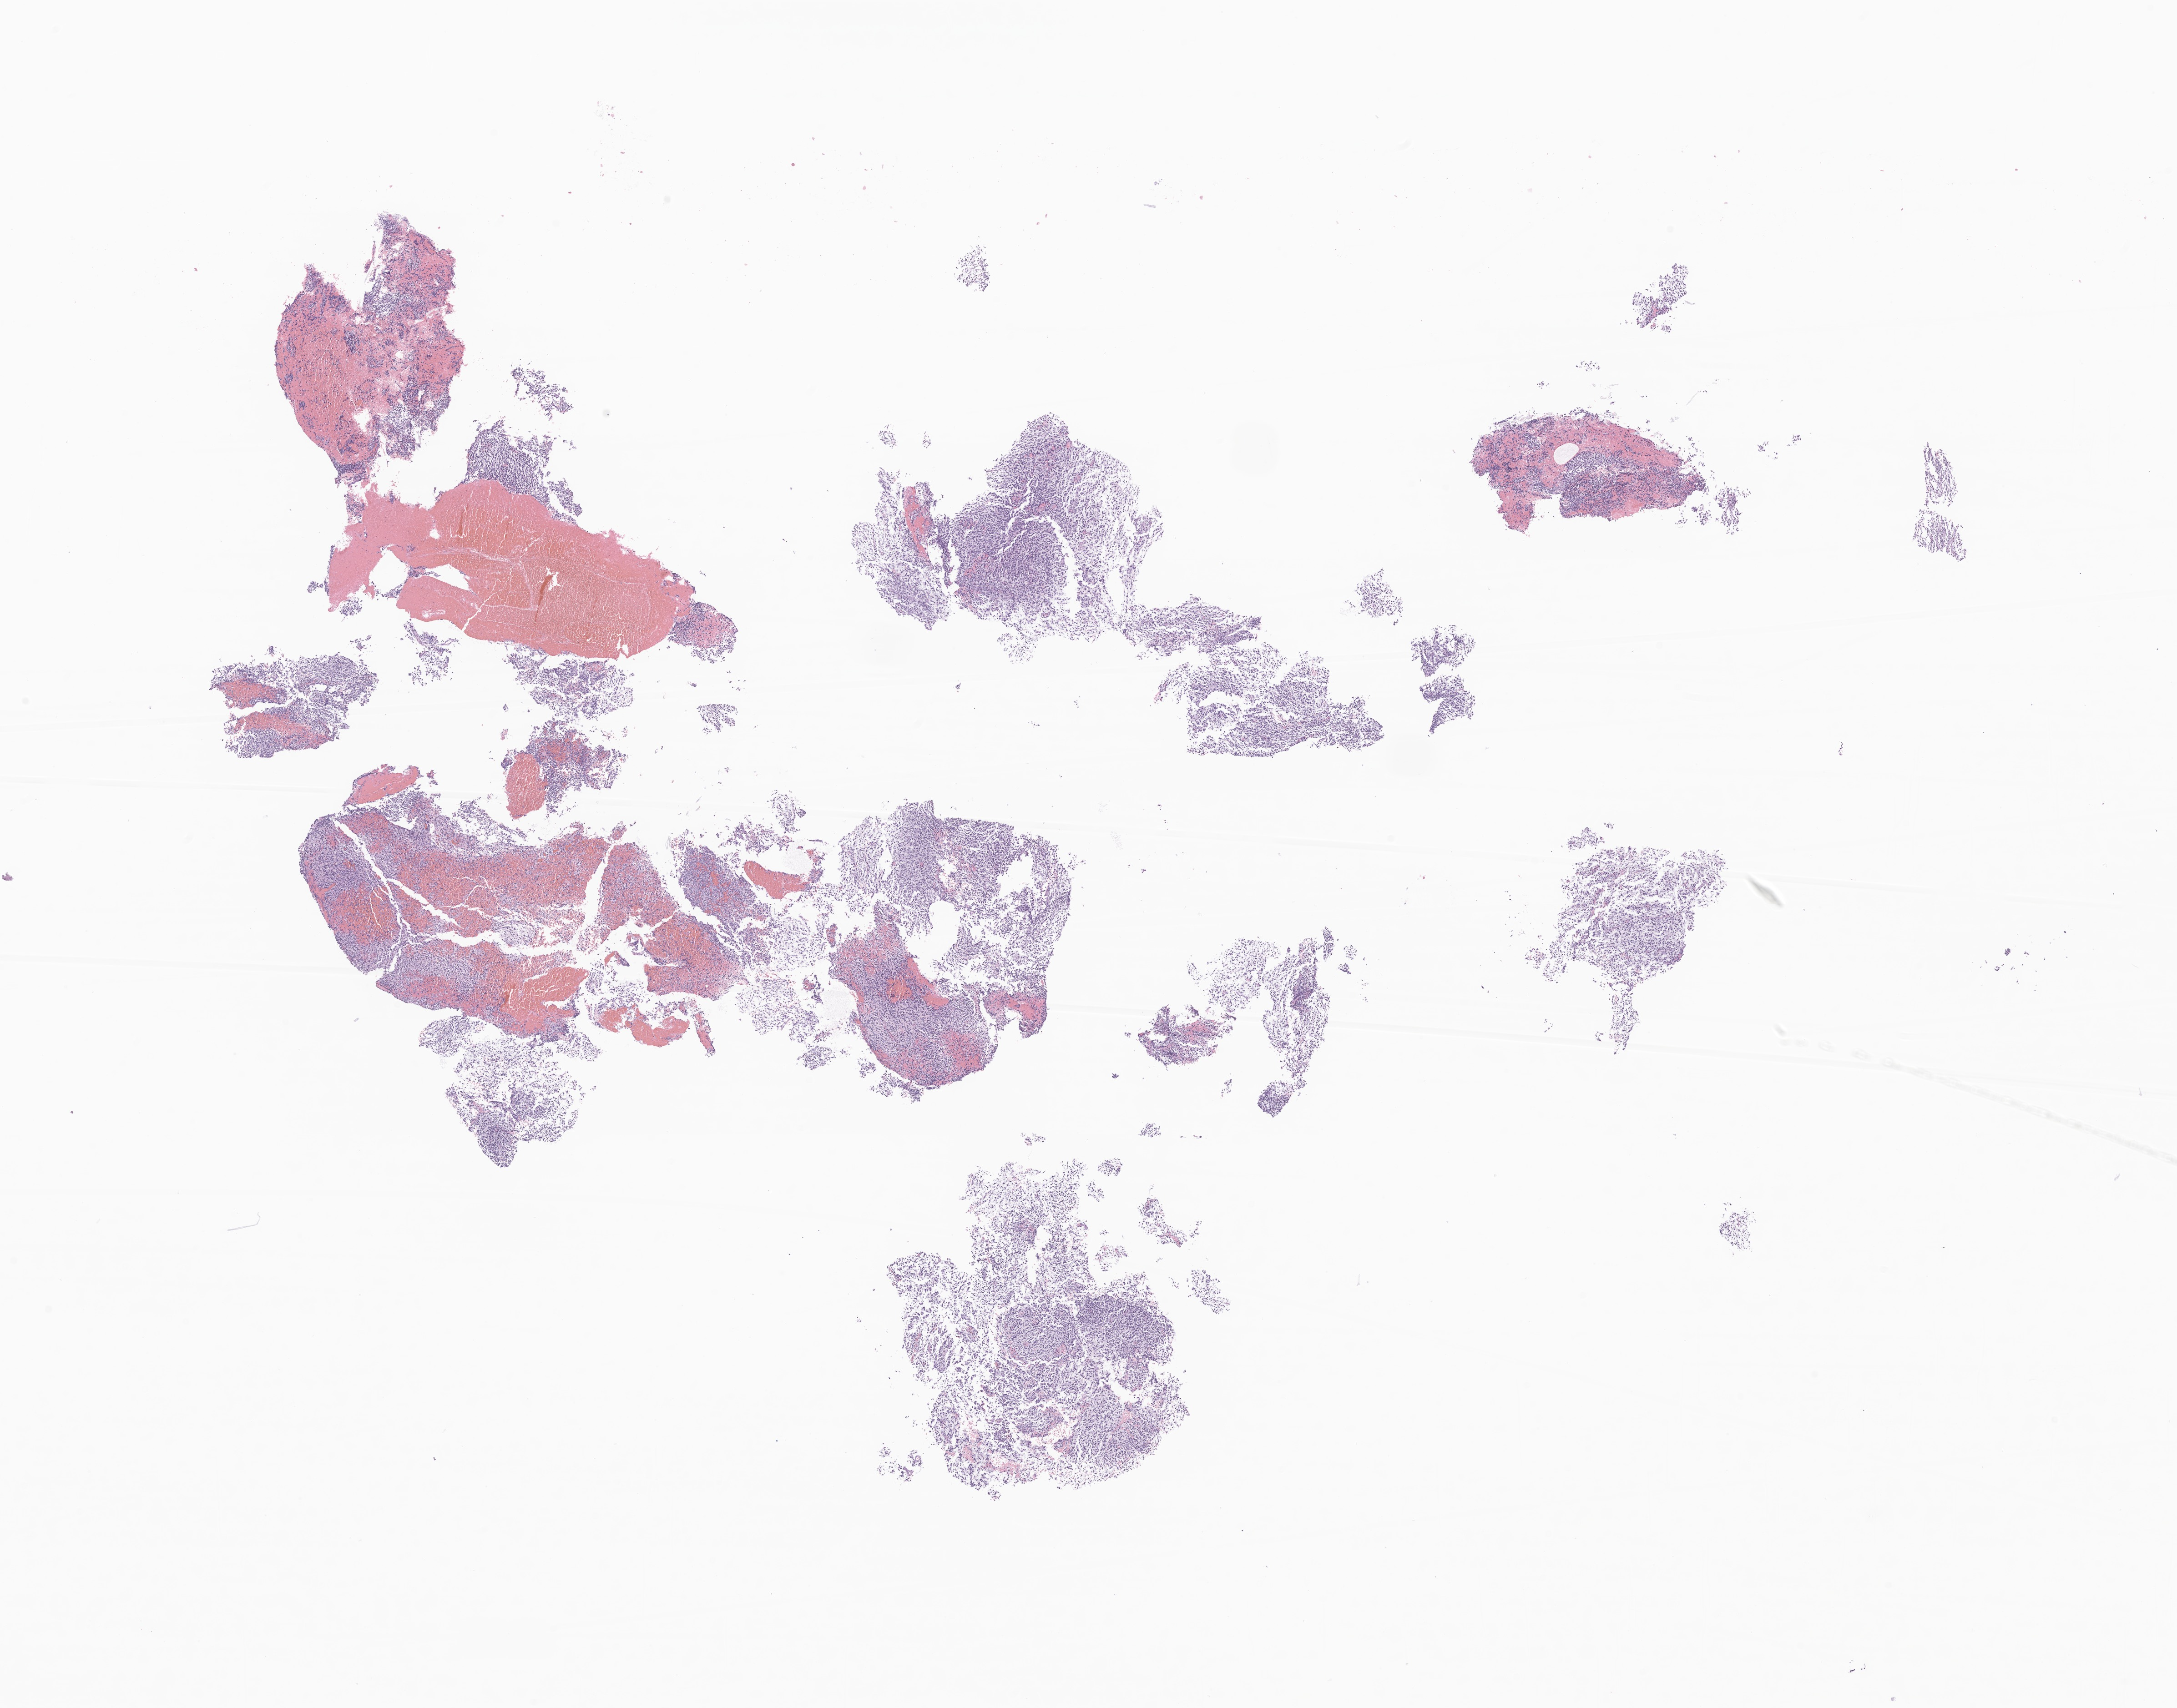
Haematoxylin and eosin whole-slide image of tumor tissue from the brain — a low-resolution overview of the entire scanned area, about 20.2 x 15.8 mm. FFPE section. Male patient, age 123 months (10 years 3 months).
• recorded diagnosis: Glioma, malignant